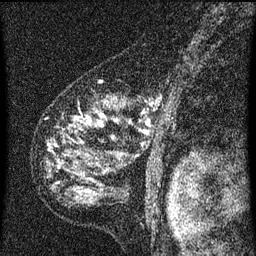
Breast MRI (dynamic contrast-enhanced), one sagittal slice. Position 42 of 60 along the scan axis. Dynamic contrast-enhanced series, image 2 of 3 at this slice position (ordered by acquisition). 1.5 T. TE 4.2 ms, TR 8 ms. 256 × 256 image matrix, field of view 180 × 180 mm. Female patient, age 55 years.
Outlined on this slice (semi-automatic segmentation, software-assisted and operator-edited):
- analysis volume of interest (the breast-tissue region the enhancement analysis was run in; not a lesion): bounding box <47,96,177,155> (left, top, right, bottom; pixels)
- tumour enhancement mask (voxels above the 70 % enhancement threshold inside the analysis volume of interest): <88,120,92,123>